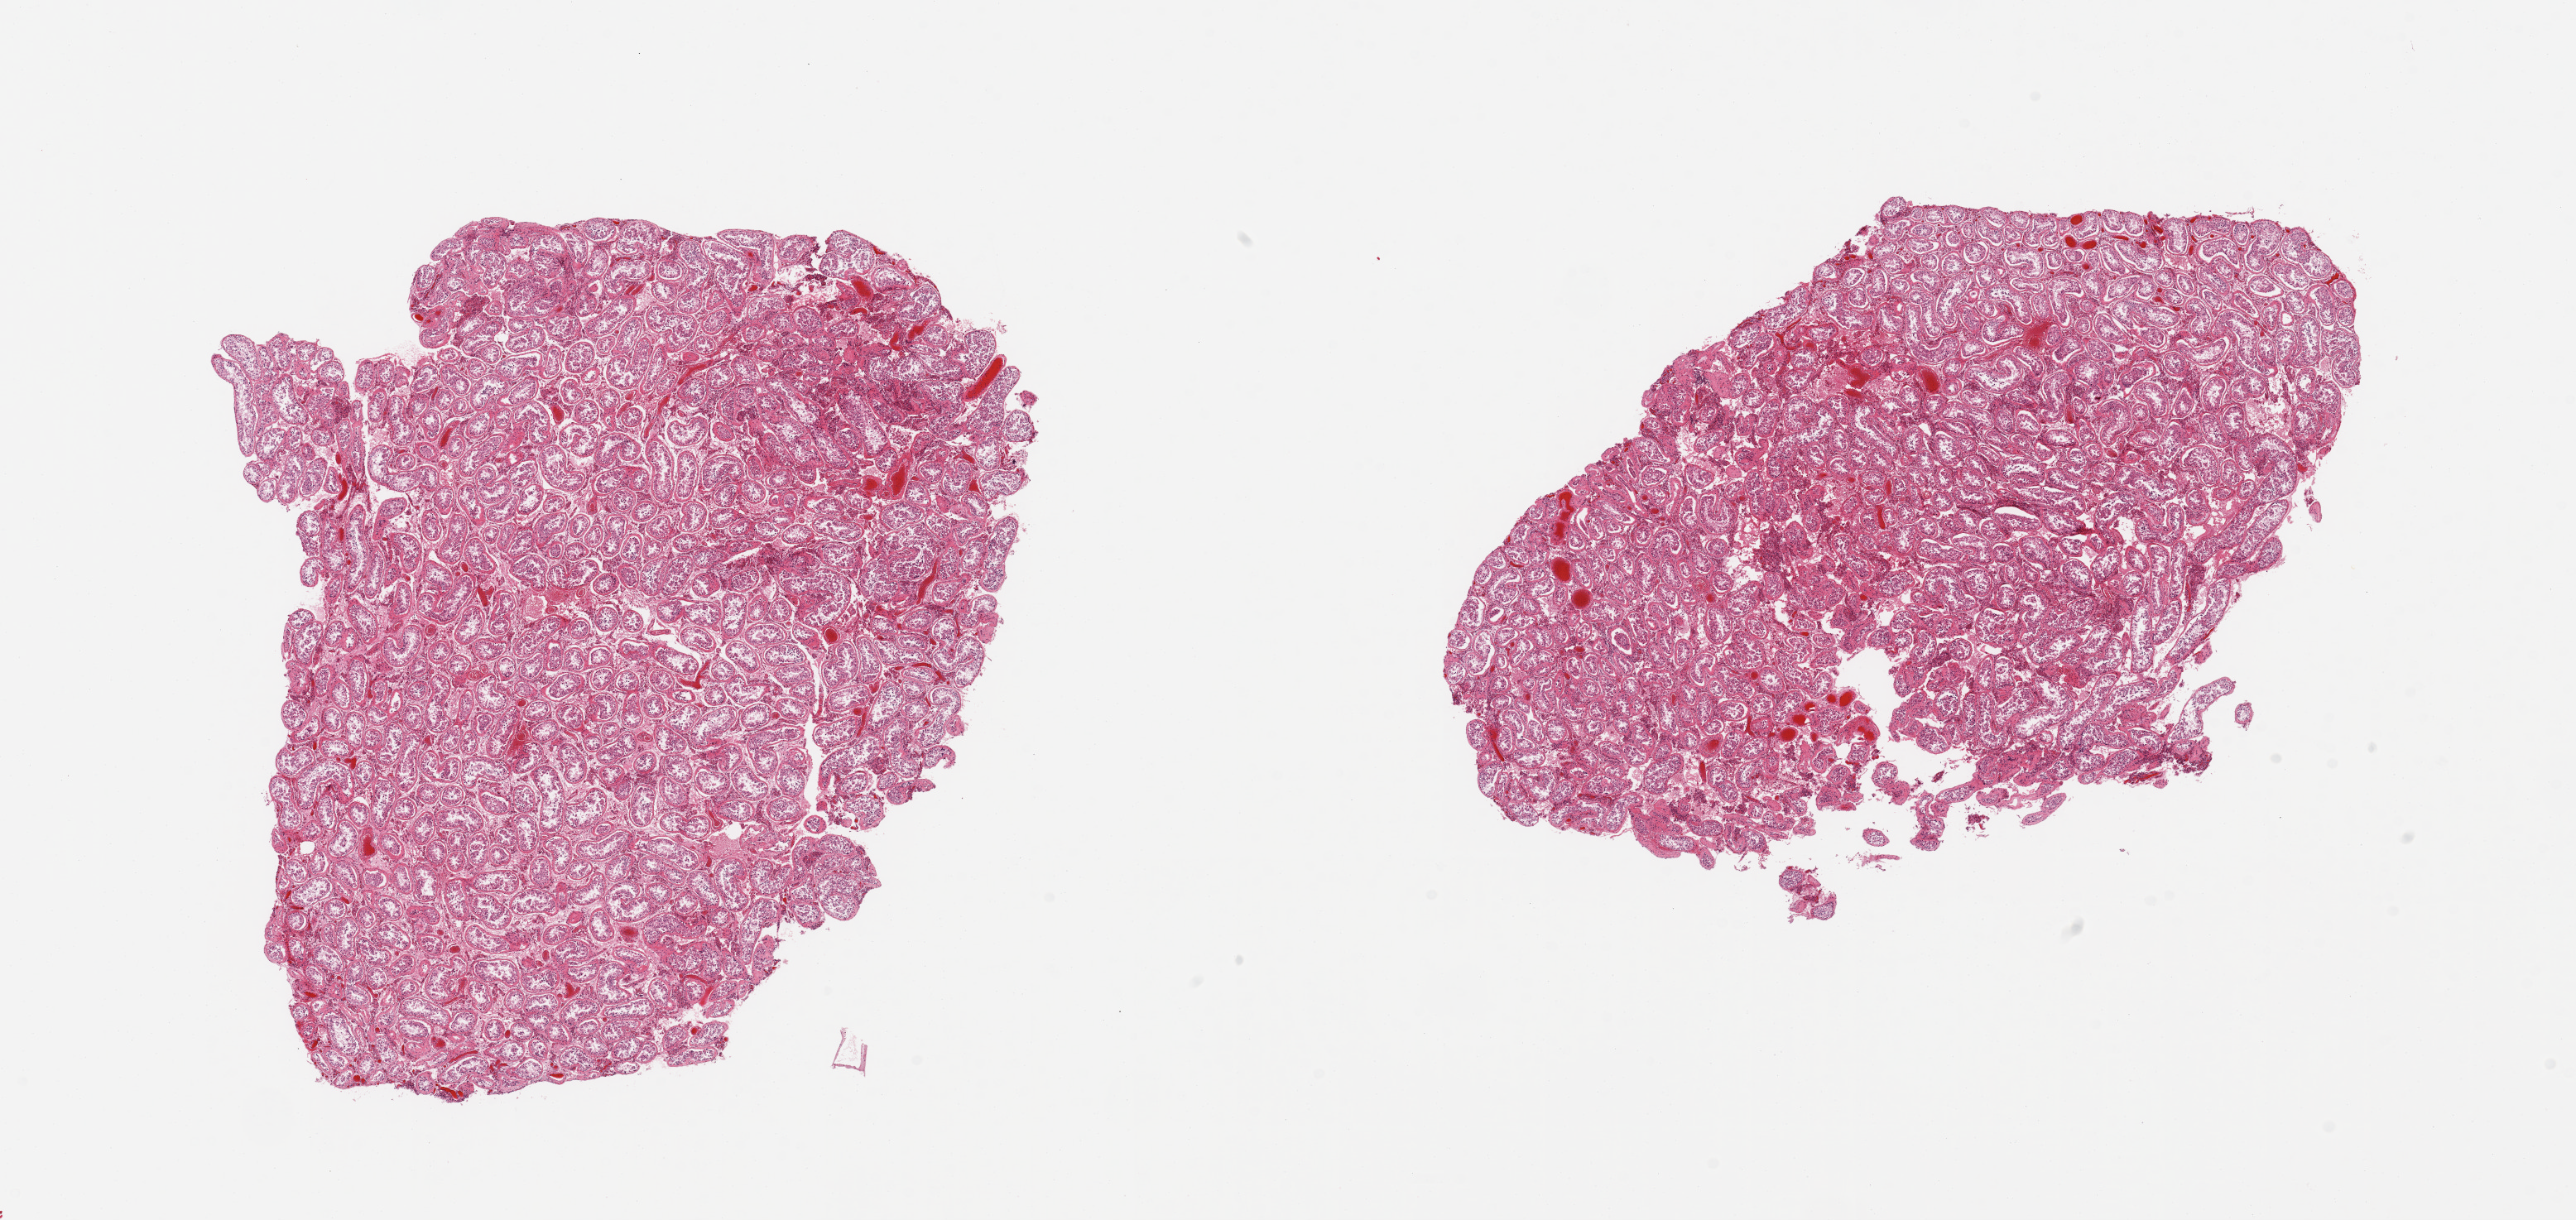
Digitized haematoxylin and eosin-stained section, brightfield — a low-resolution overview of the entire scanned area, about 24.6 x 11.7 mm (slide scanned at 20x). PAXgene-fixed, paraffin-embedded tissue. Target tissue: testis. Donor tissue sample. Male donor.
Pathologist's review note for this sample: 2 pieces; Sertoli cells, reduced/absent spermatogenesis, increased Leydig cells, c/w atrophy, congestion.